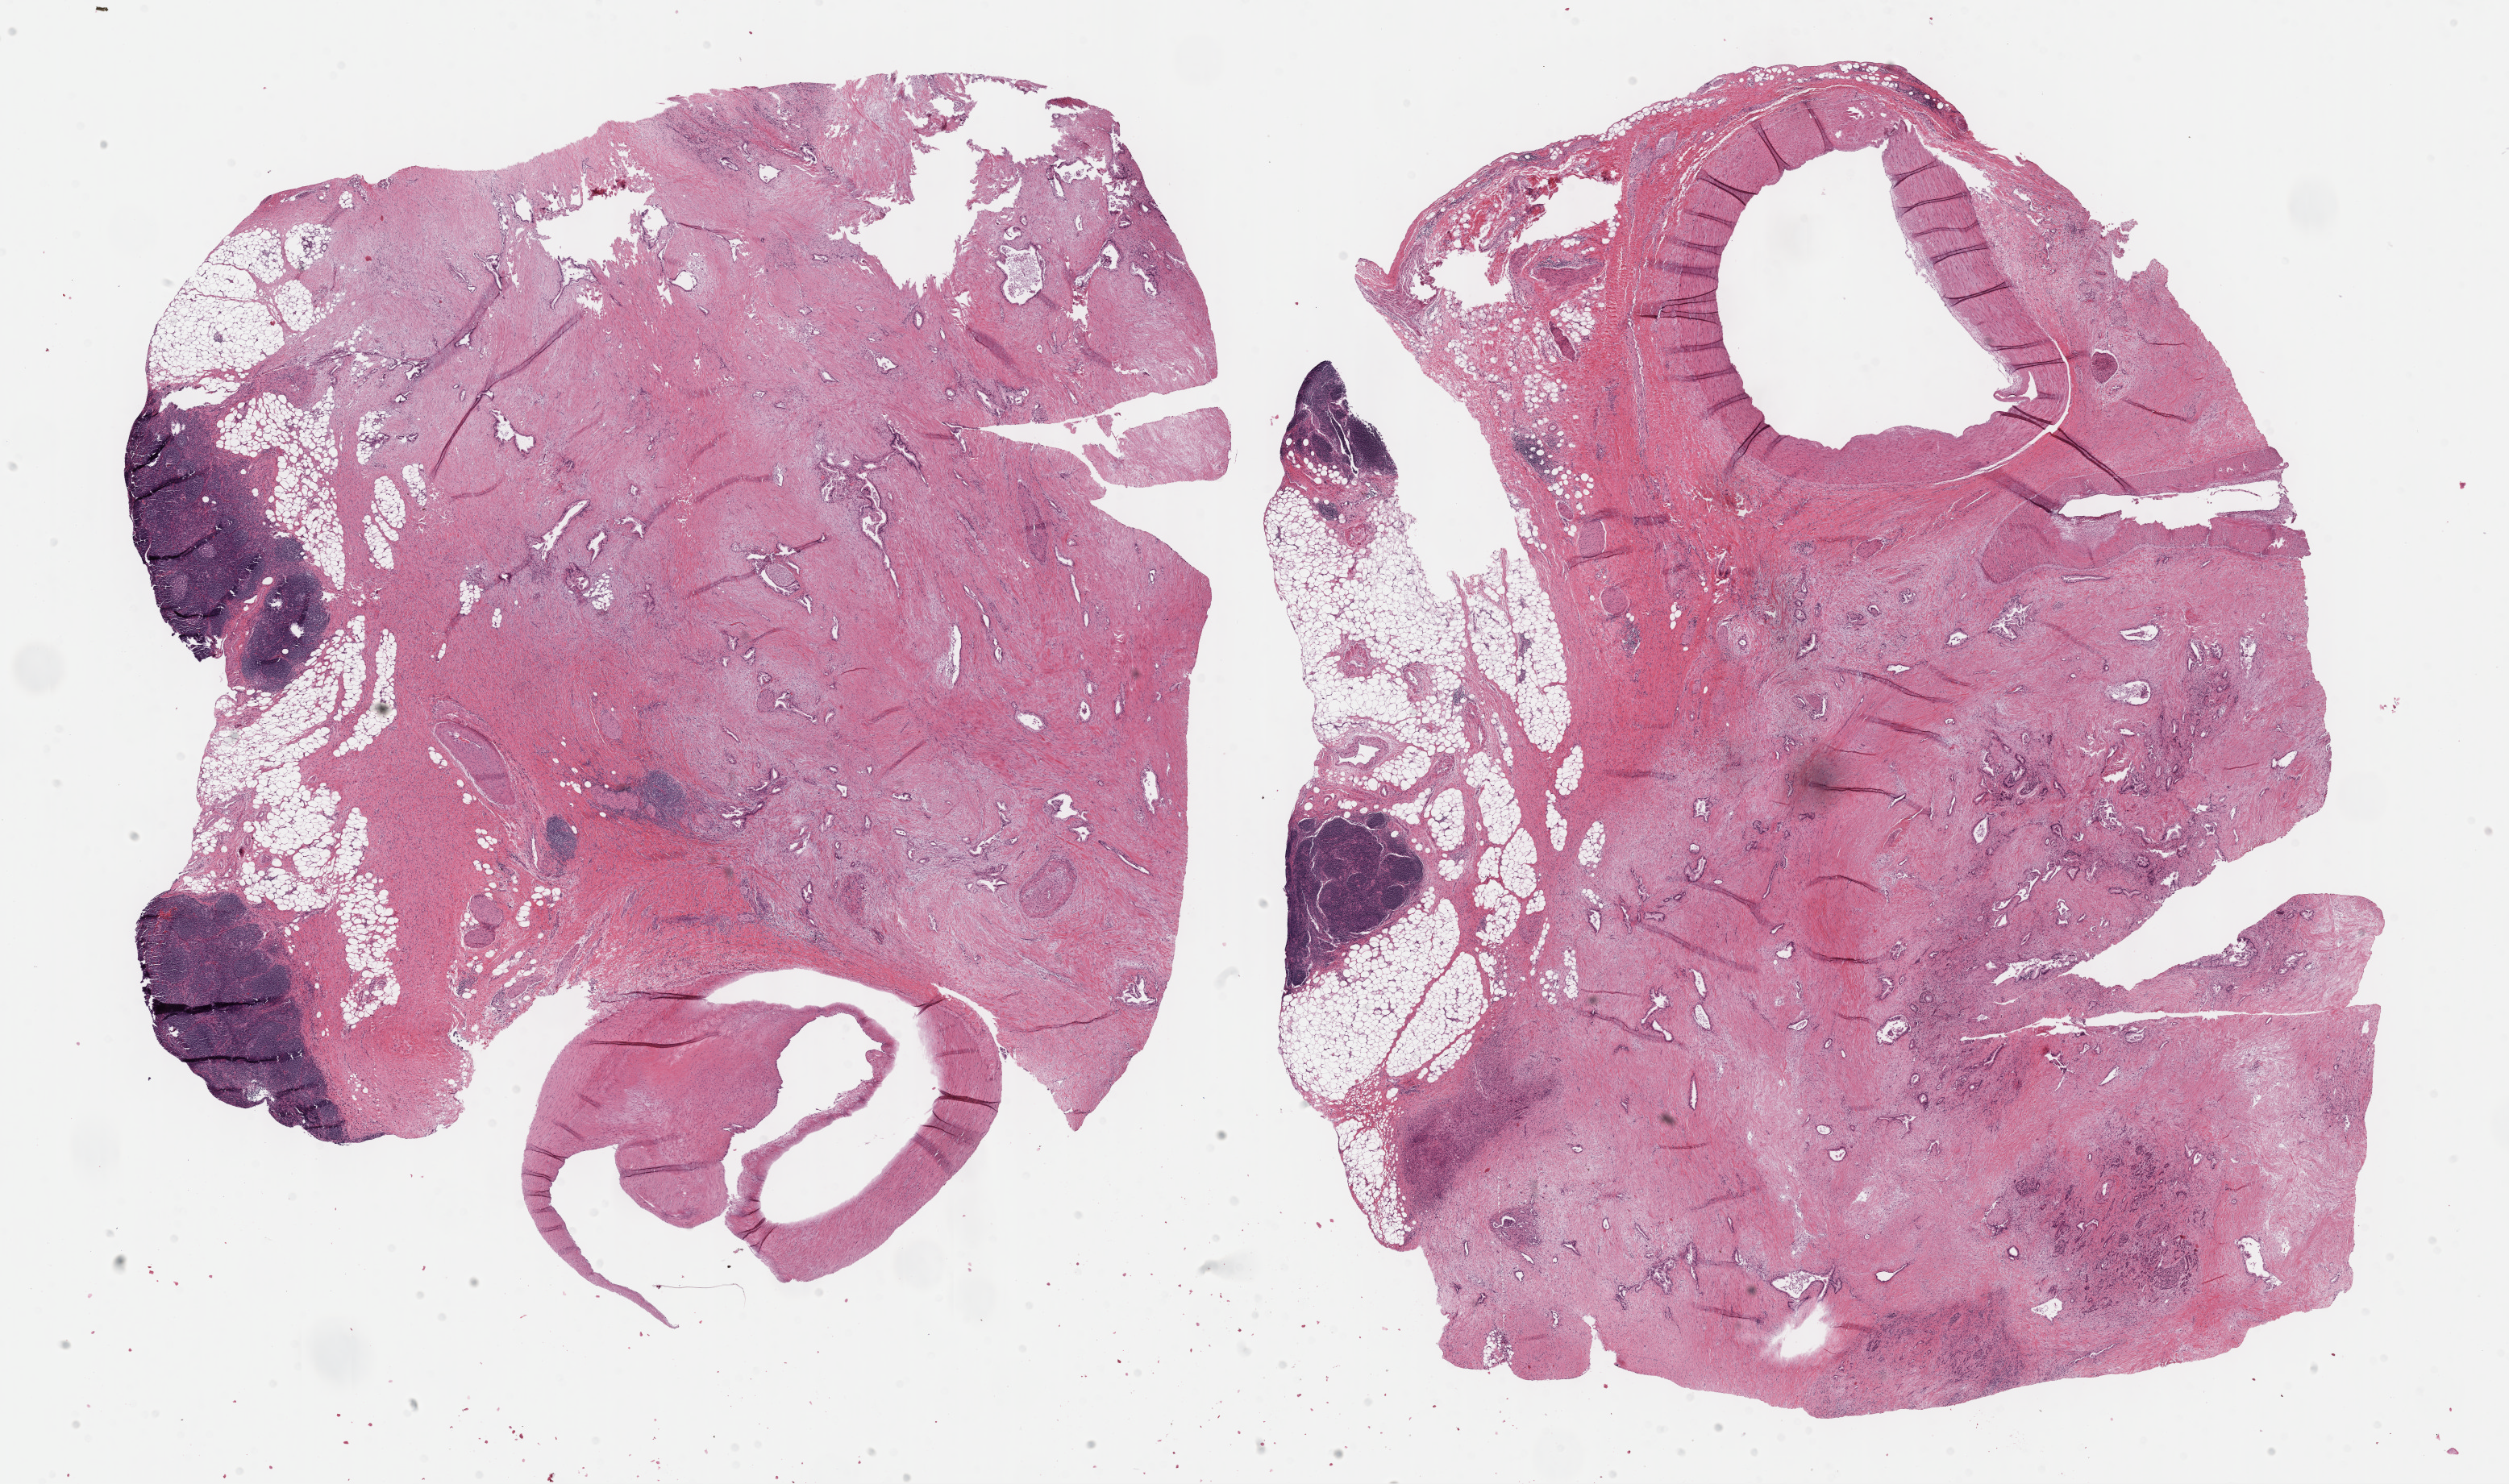
H&E whole-slide image, low-resolution overview of the scanned area, about 25.2 x 14.9 mm. Formalin-fixed paraffin-embedded (FFPE) diagnostic section. Pancreas, primary tumour sample. Patient: male, age at initial diagnosis 48 years. Histologic grade: G2 (moderately differentiated).
- pathologic diagnosis: Adenocarcinoma, NOS (overlapping lesion of pancreas)
- AJCC pathologic stage: IIB (7th edition)
- lymph nodes positive (case pathology): 0 of 34 examined